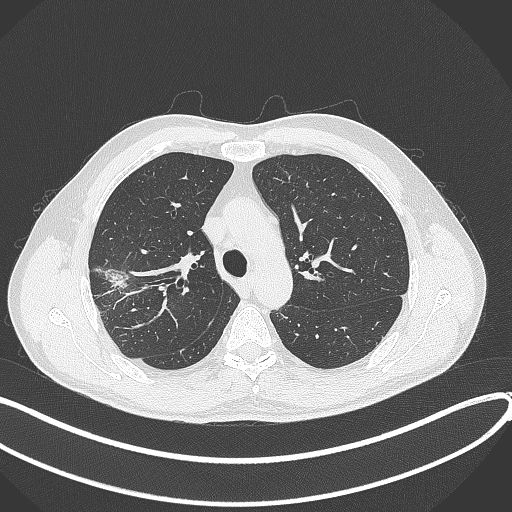
Chest CT, one axial slice. Slice 299 of 381 in the series (ordered by position). Reconstruction kernel B70f. 120 kVp. Lung window (W 1500 / L -600 HU). 1 mm slice thickness. 512 × 512 image matrix, field of view 400 × 400 mm. Male patient, age 62 years. From the clinical record (not read from this slice): clinical TNM (as recorded): T1c N0 M0.
Outlined on this slice (bounding box drawn by a radiologist):
- lung tumour (recorded histology: adenocarcinoma): box from (x=105, y=264) to (x=130, y=293) px